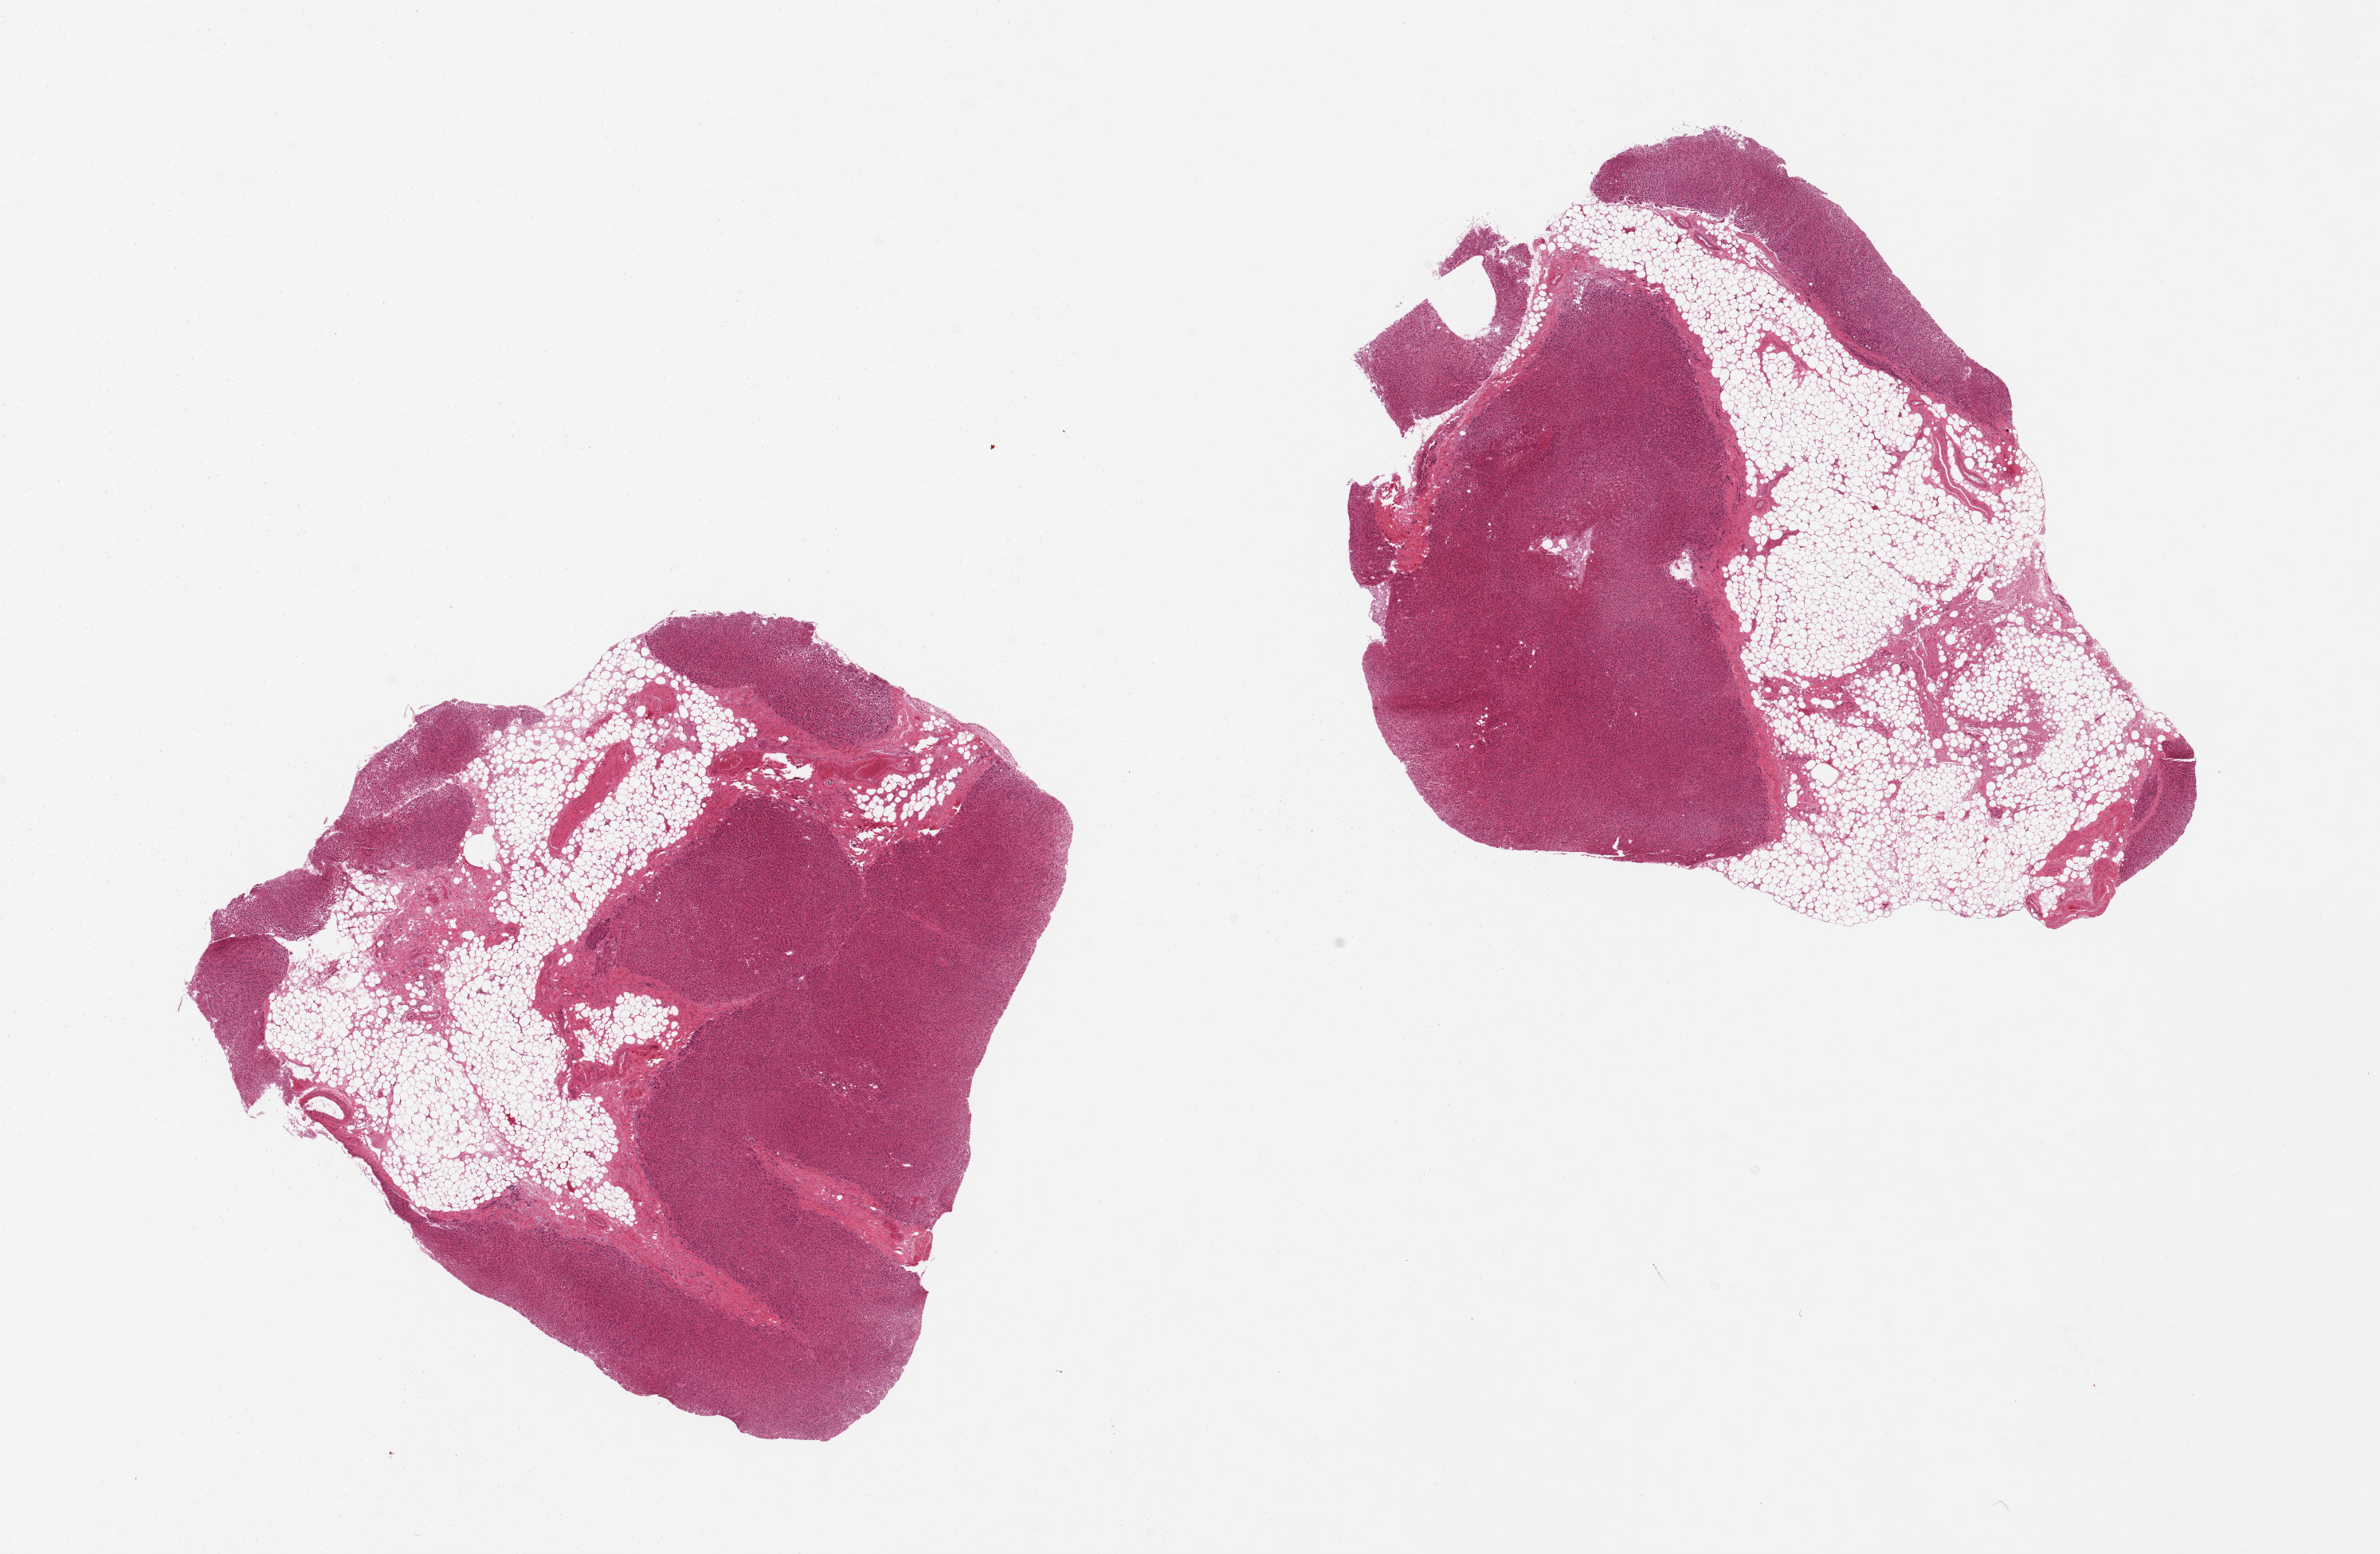
Hematoxylin and eosin (H&E) whole-slide image, shown as a low-resolution overview of the whole scanned area (about 23.6 x 15.4 mm). PAXgene-fixed paraffin-embedded (PFPE) section. Target tissue: adrenal gland. Donor tissue sample. Donor: male.
Pathologist's review note for this sample: 2 pieces,autolyzed cortex; both aliquots 40-50% adipose tissue.